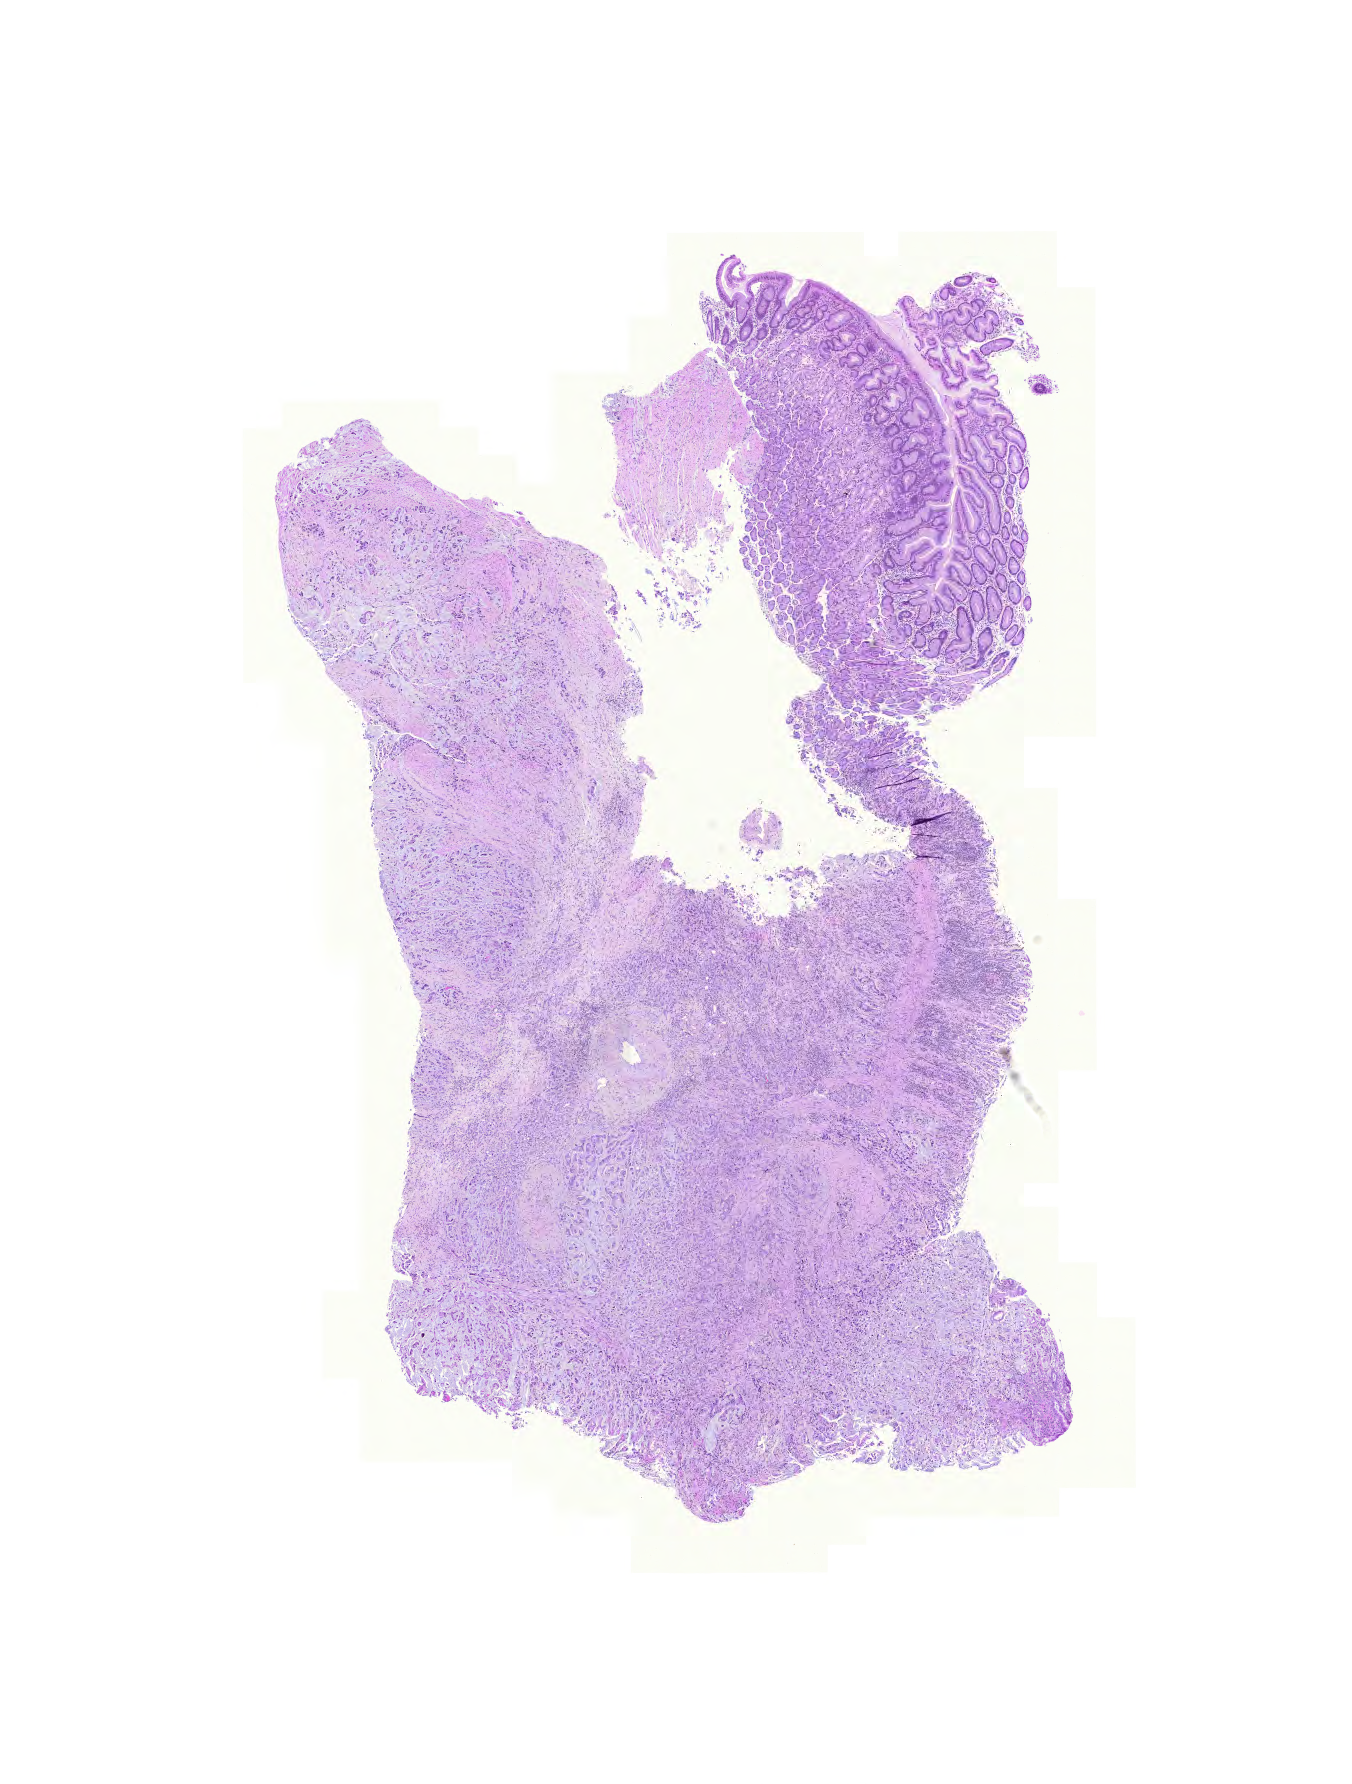
Digitized Hematoxylin and eosin (H&E) stained tissue section (whole slide) — shown as a low-resolution overview of the whole scanned area (about 10.1 x 13.3 mm); FFPE section; sample: primary tumour, stomach. Male patient; age at initial diagnosis 76 years. Histologic grade: G3 (poorly differentiated).
• diagnosis: Adenocarcinoma with mixed subtypes
• AJCC pathologic stage: IIB (7th edition)
• lymph nodes positive (case pathology): 2 of 20 examined